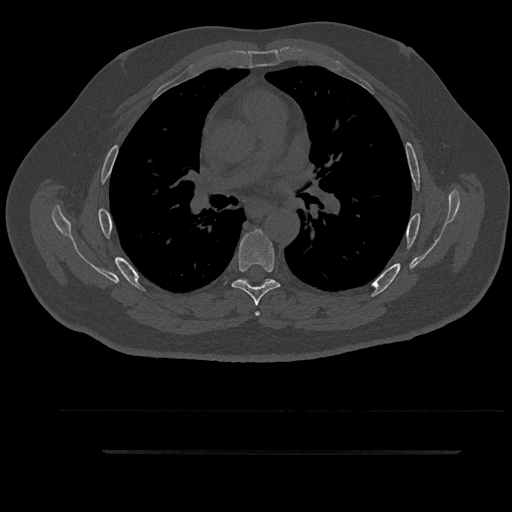
CT including the spine, one axial slice; slice 577 of 797 in the series (ordered by position); reconstruction kernel Br40s/3; 120 kVp; bone window (W 1800 / L 400 HU); 512 × 512 image matrix, field of view 432 × 432 mm. Patient: male, 63 years. Case-level facts recorded for this patient, not image findings: primary cancer: renal; vertebrae with lytic lesions (as recorded): T8.
Annotated regions visible in this slice (semi-automatic segmentation, software-assisted and operator-edited):
- T5 vertebra: bounding box (x1, y1, x2, y2) in pixels: (238, 278, 272, 316)
- T6 vertebra: (232, 229, 281, 306)